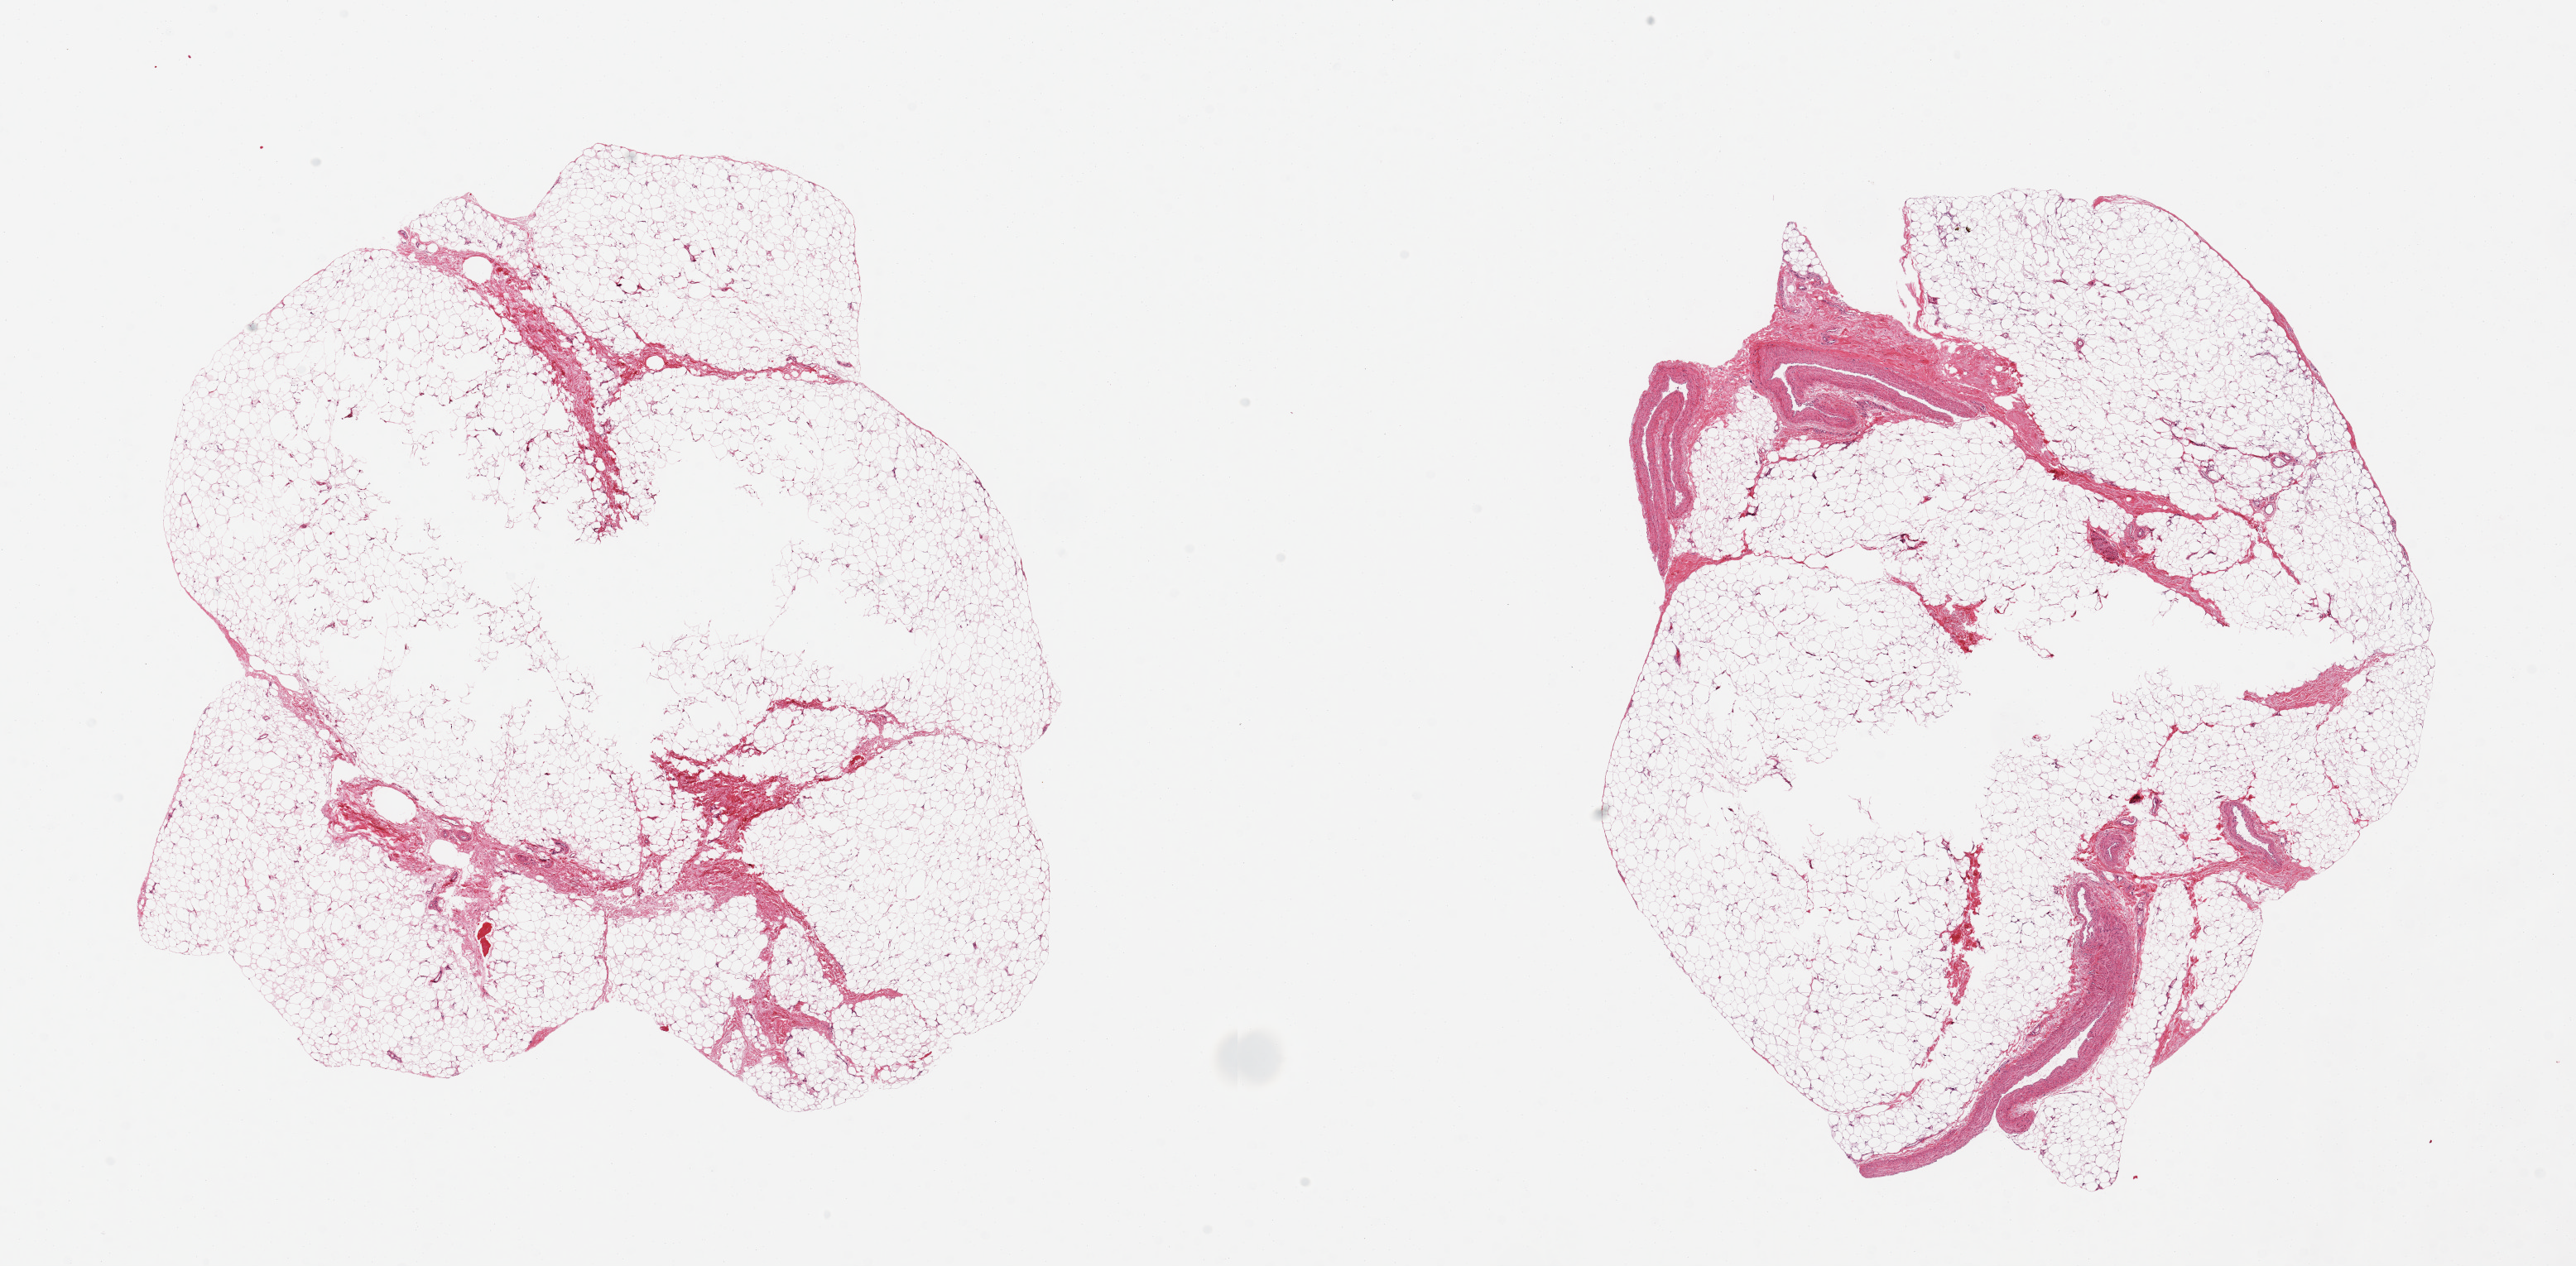
H&E whole-slide image, brightfield, a low-resolution overview of the entire scanned area, about 24.6 x 12.1 mm. PAXgene-fixed paraffin-embedded (PFPE) section. Target tissue: adipose tissue. Tissue donor sample. Donor: male.
• reviewer comment on this tissue sample: 2 pieces 9x8 & 8x7 mm; holes in central 20%